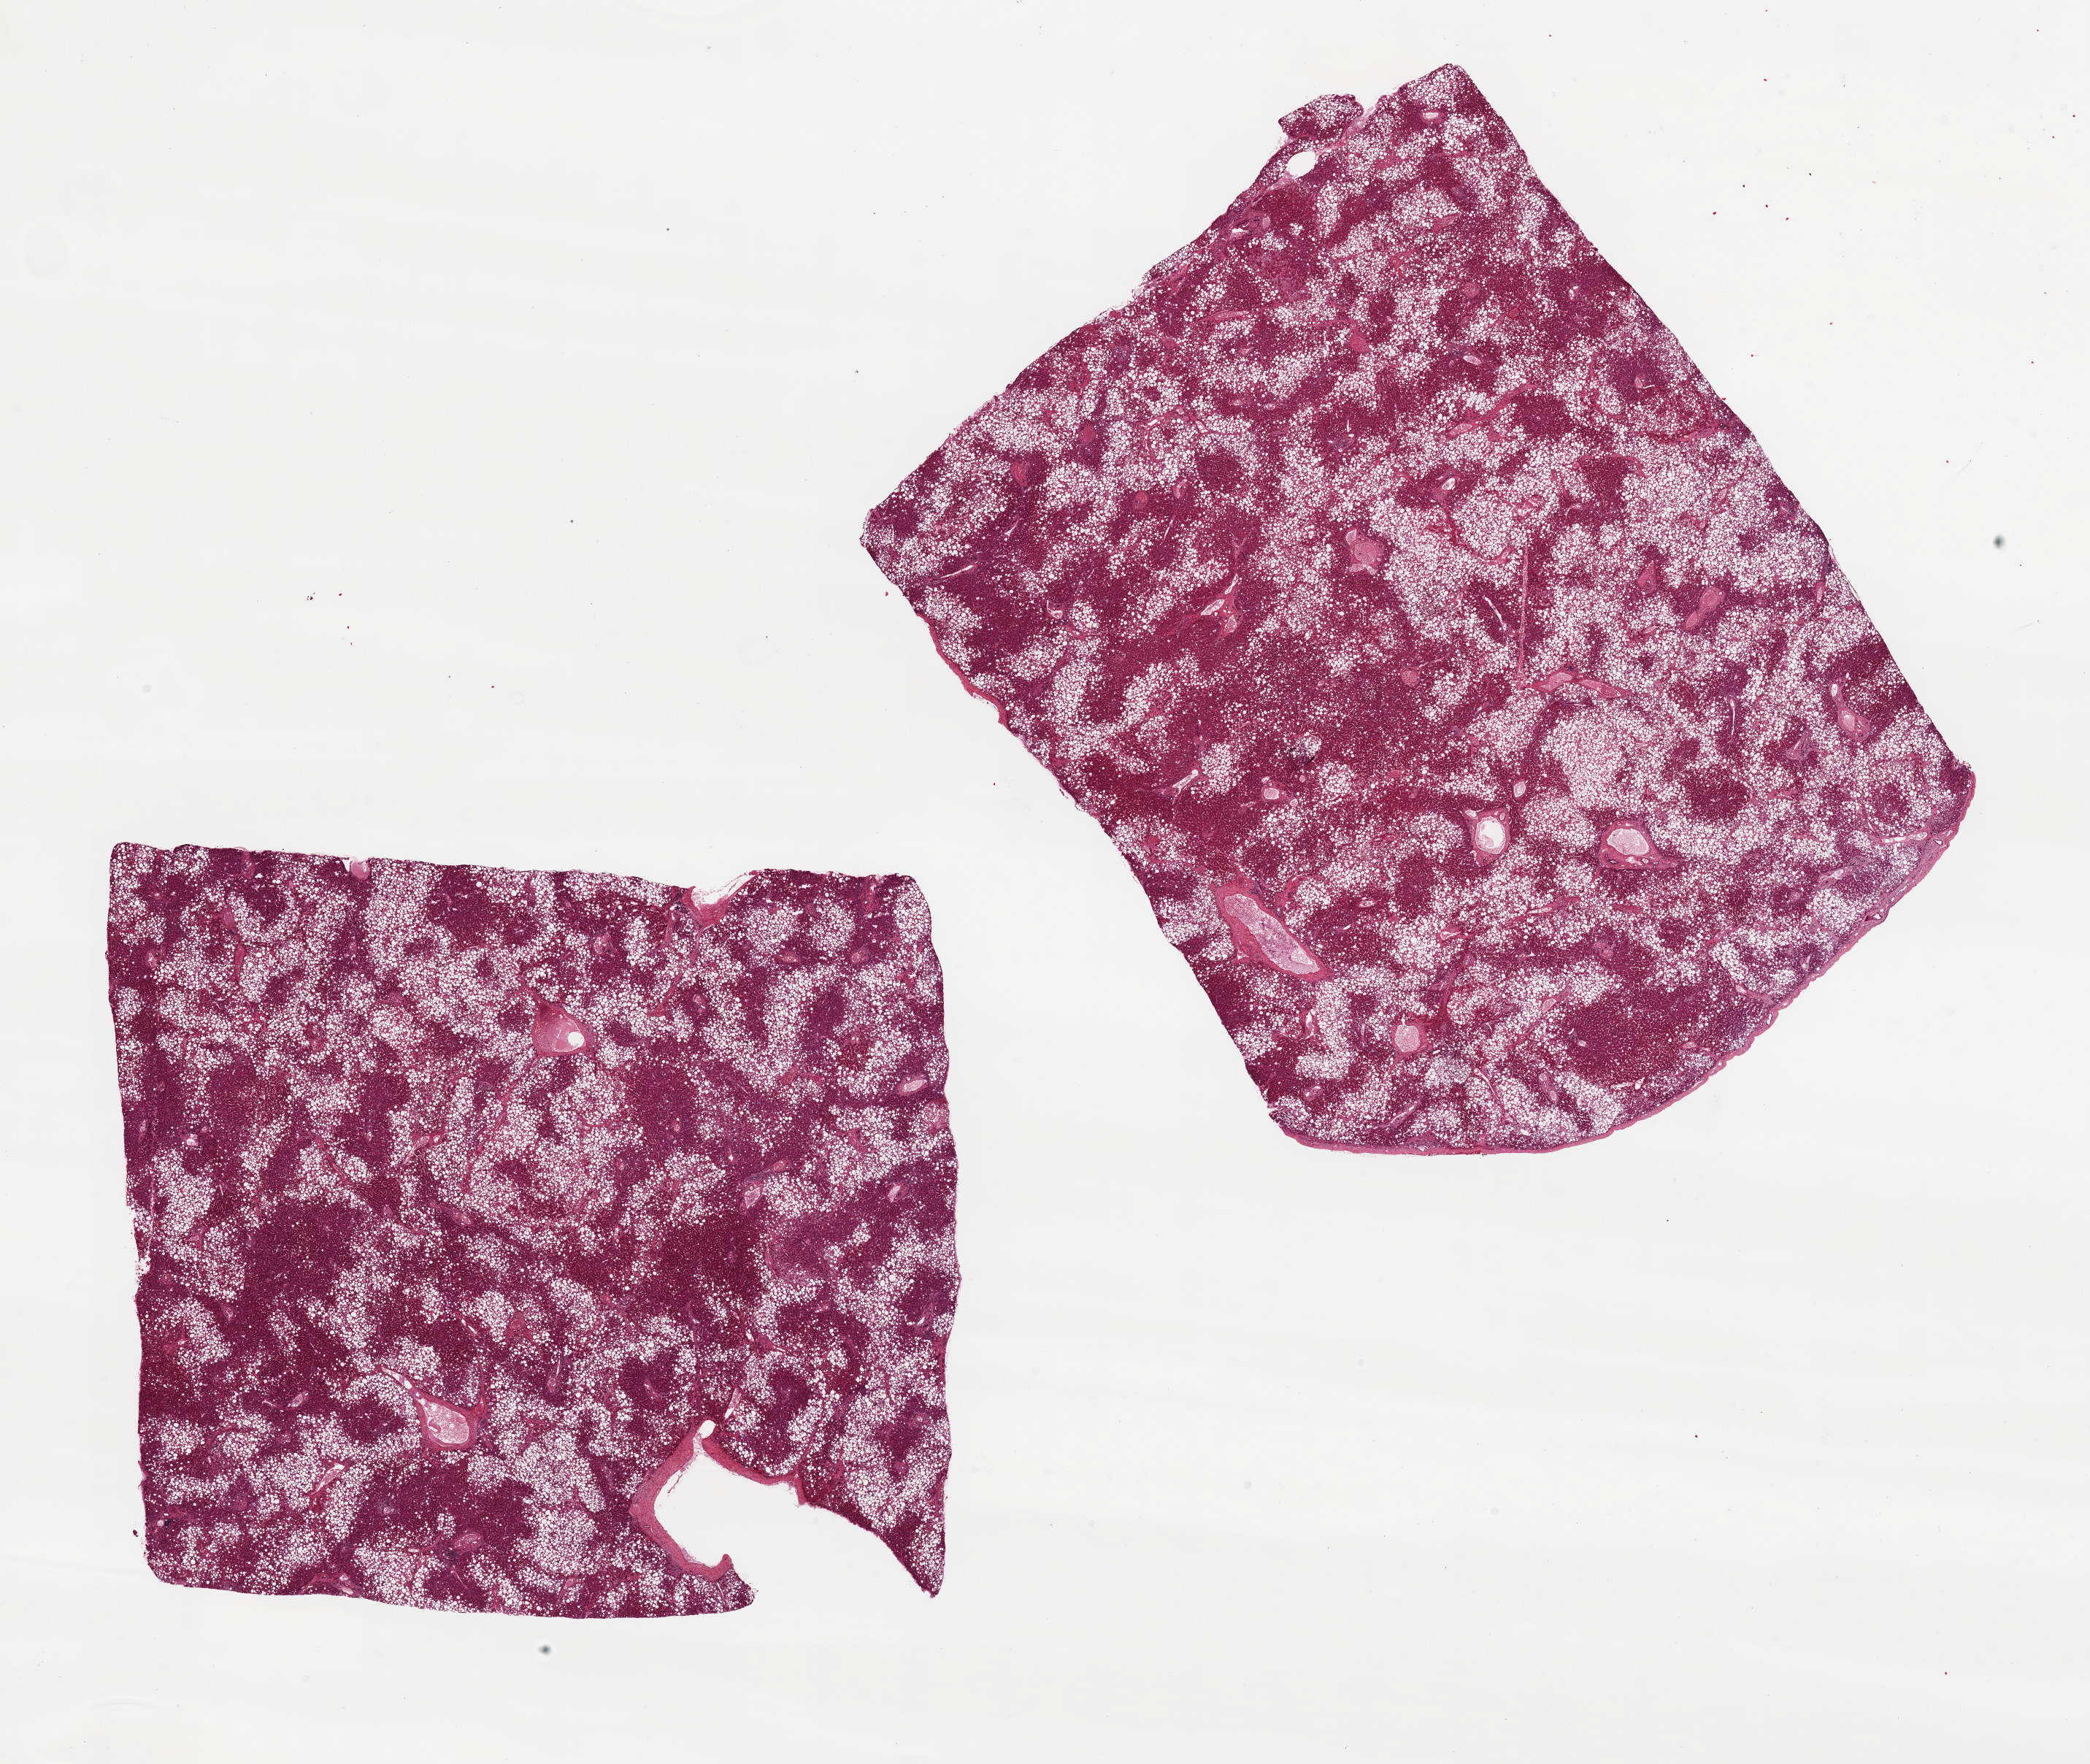
Hematoxylin and eosin (H&E) whole-slide image — shown as a low-resolution overview of the whole scanned area (about 22.6 x 19.1 mm). PAXgene-fixed, paraffin-embedded tissue. Target tissue: liver. Tissue donor sample. Male donor.
Review note (as recorded): 2 aliquots, ~9x9mm, diffuse macrovesicular steatosis involves 80+% of parenchyma.